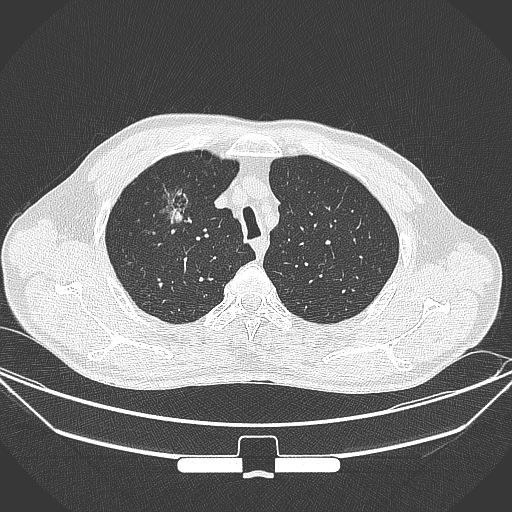
Chest CT, one axial slice; slice 281 of 355 in the series (ordered by position); 120 kVp; lung window (W 1500 / L -600 HU); 512 × 512 image matrix, field of view 399 × 399 mm. Patient: male, 67 years. From the clinical record (not read from this slice): clinical TNM (as recorded): T1c N0 M0; histopathological grade: G2.
Annotated regions visible in this slice (bounding box drawn by a radiologist):
- lung tumour (recorded histology: adenocarcinoma): box from (x=150, y=176) to (x=195, y=232) px